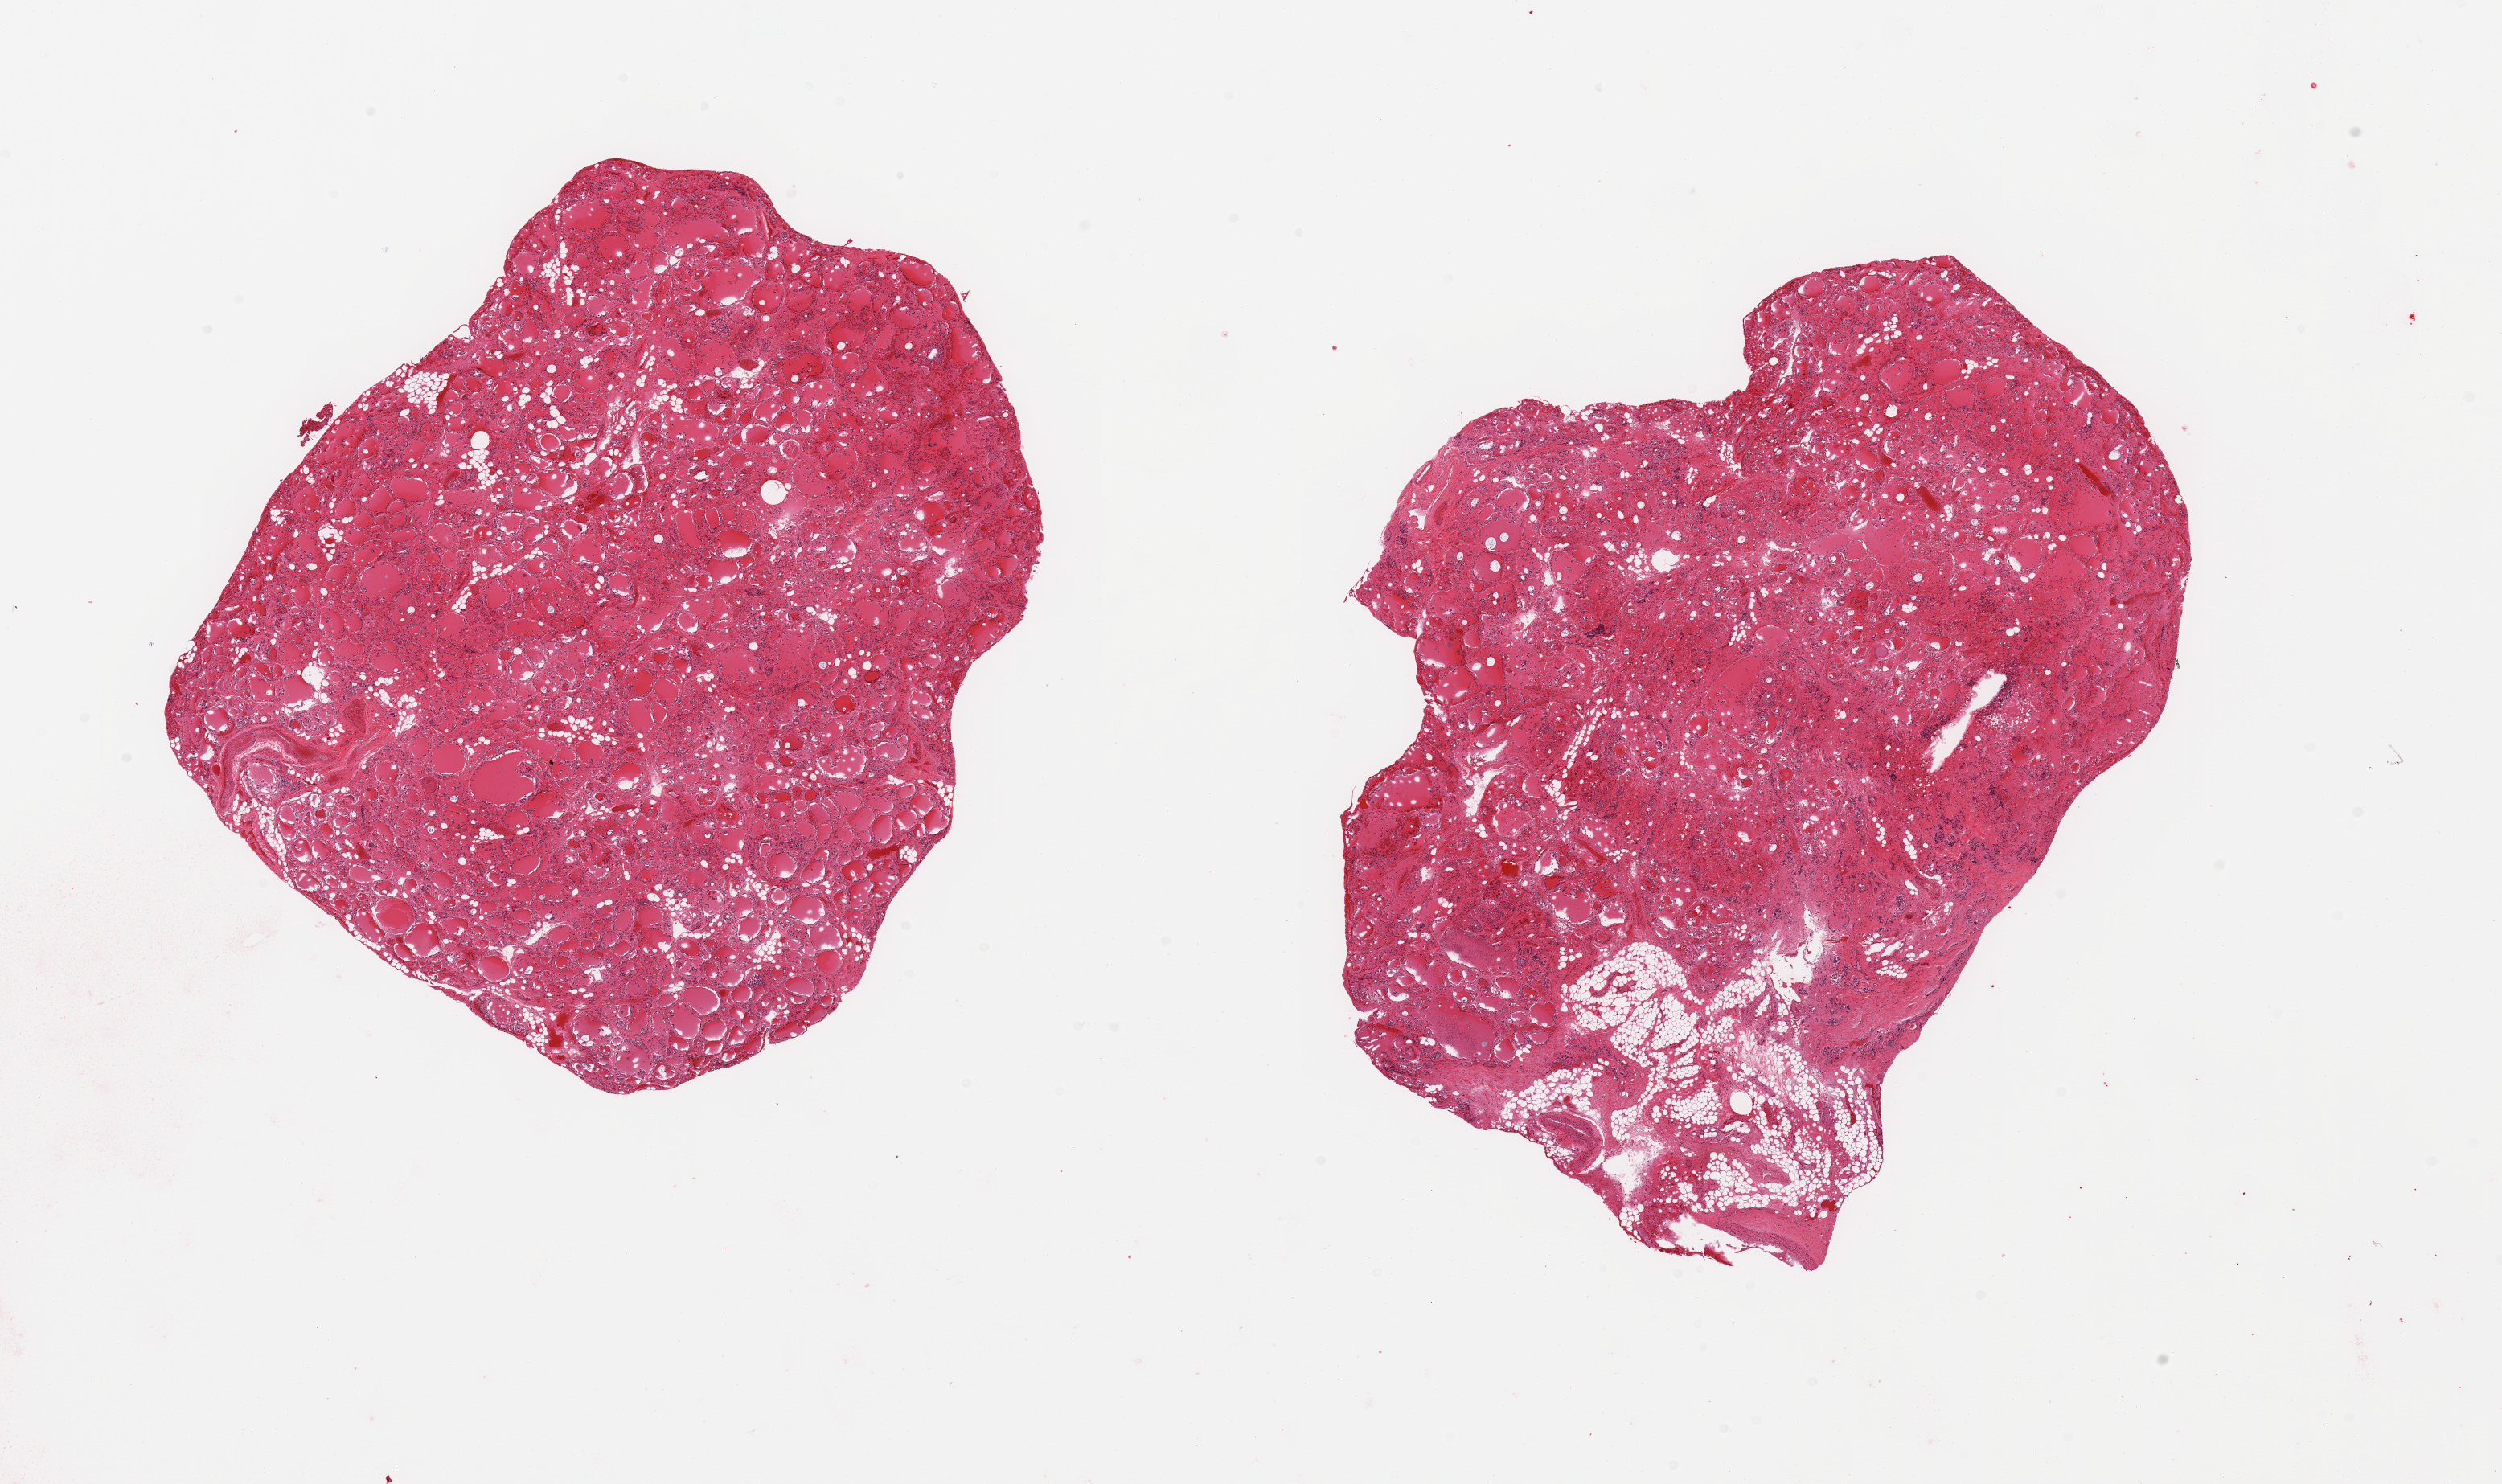
Digitized haematoxylin and eosin-stained section, brightfield — low-resolution overview of the scanned area, about 24.6 x 14.6 mm; PAXgene-fixed, paraffin-embedded tissue; target tissue: thyroid; tissue donor sample.
- review note (as recorded): 2 pieces; moderately to severely autolyzed, ~15% of 1 piece is fat/vessels